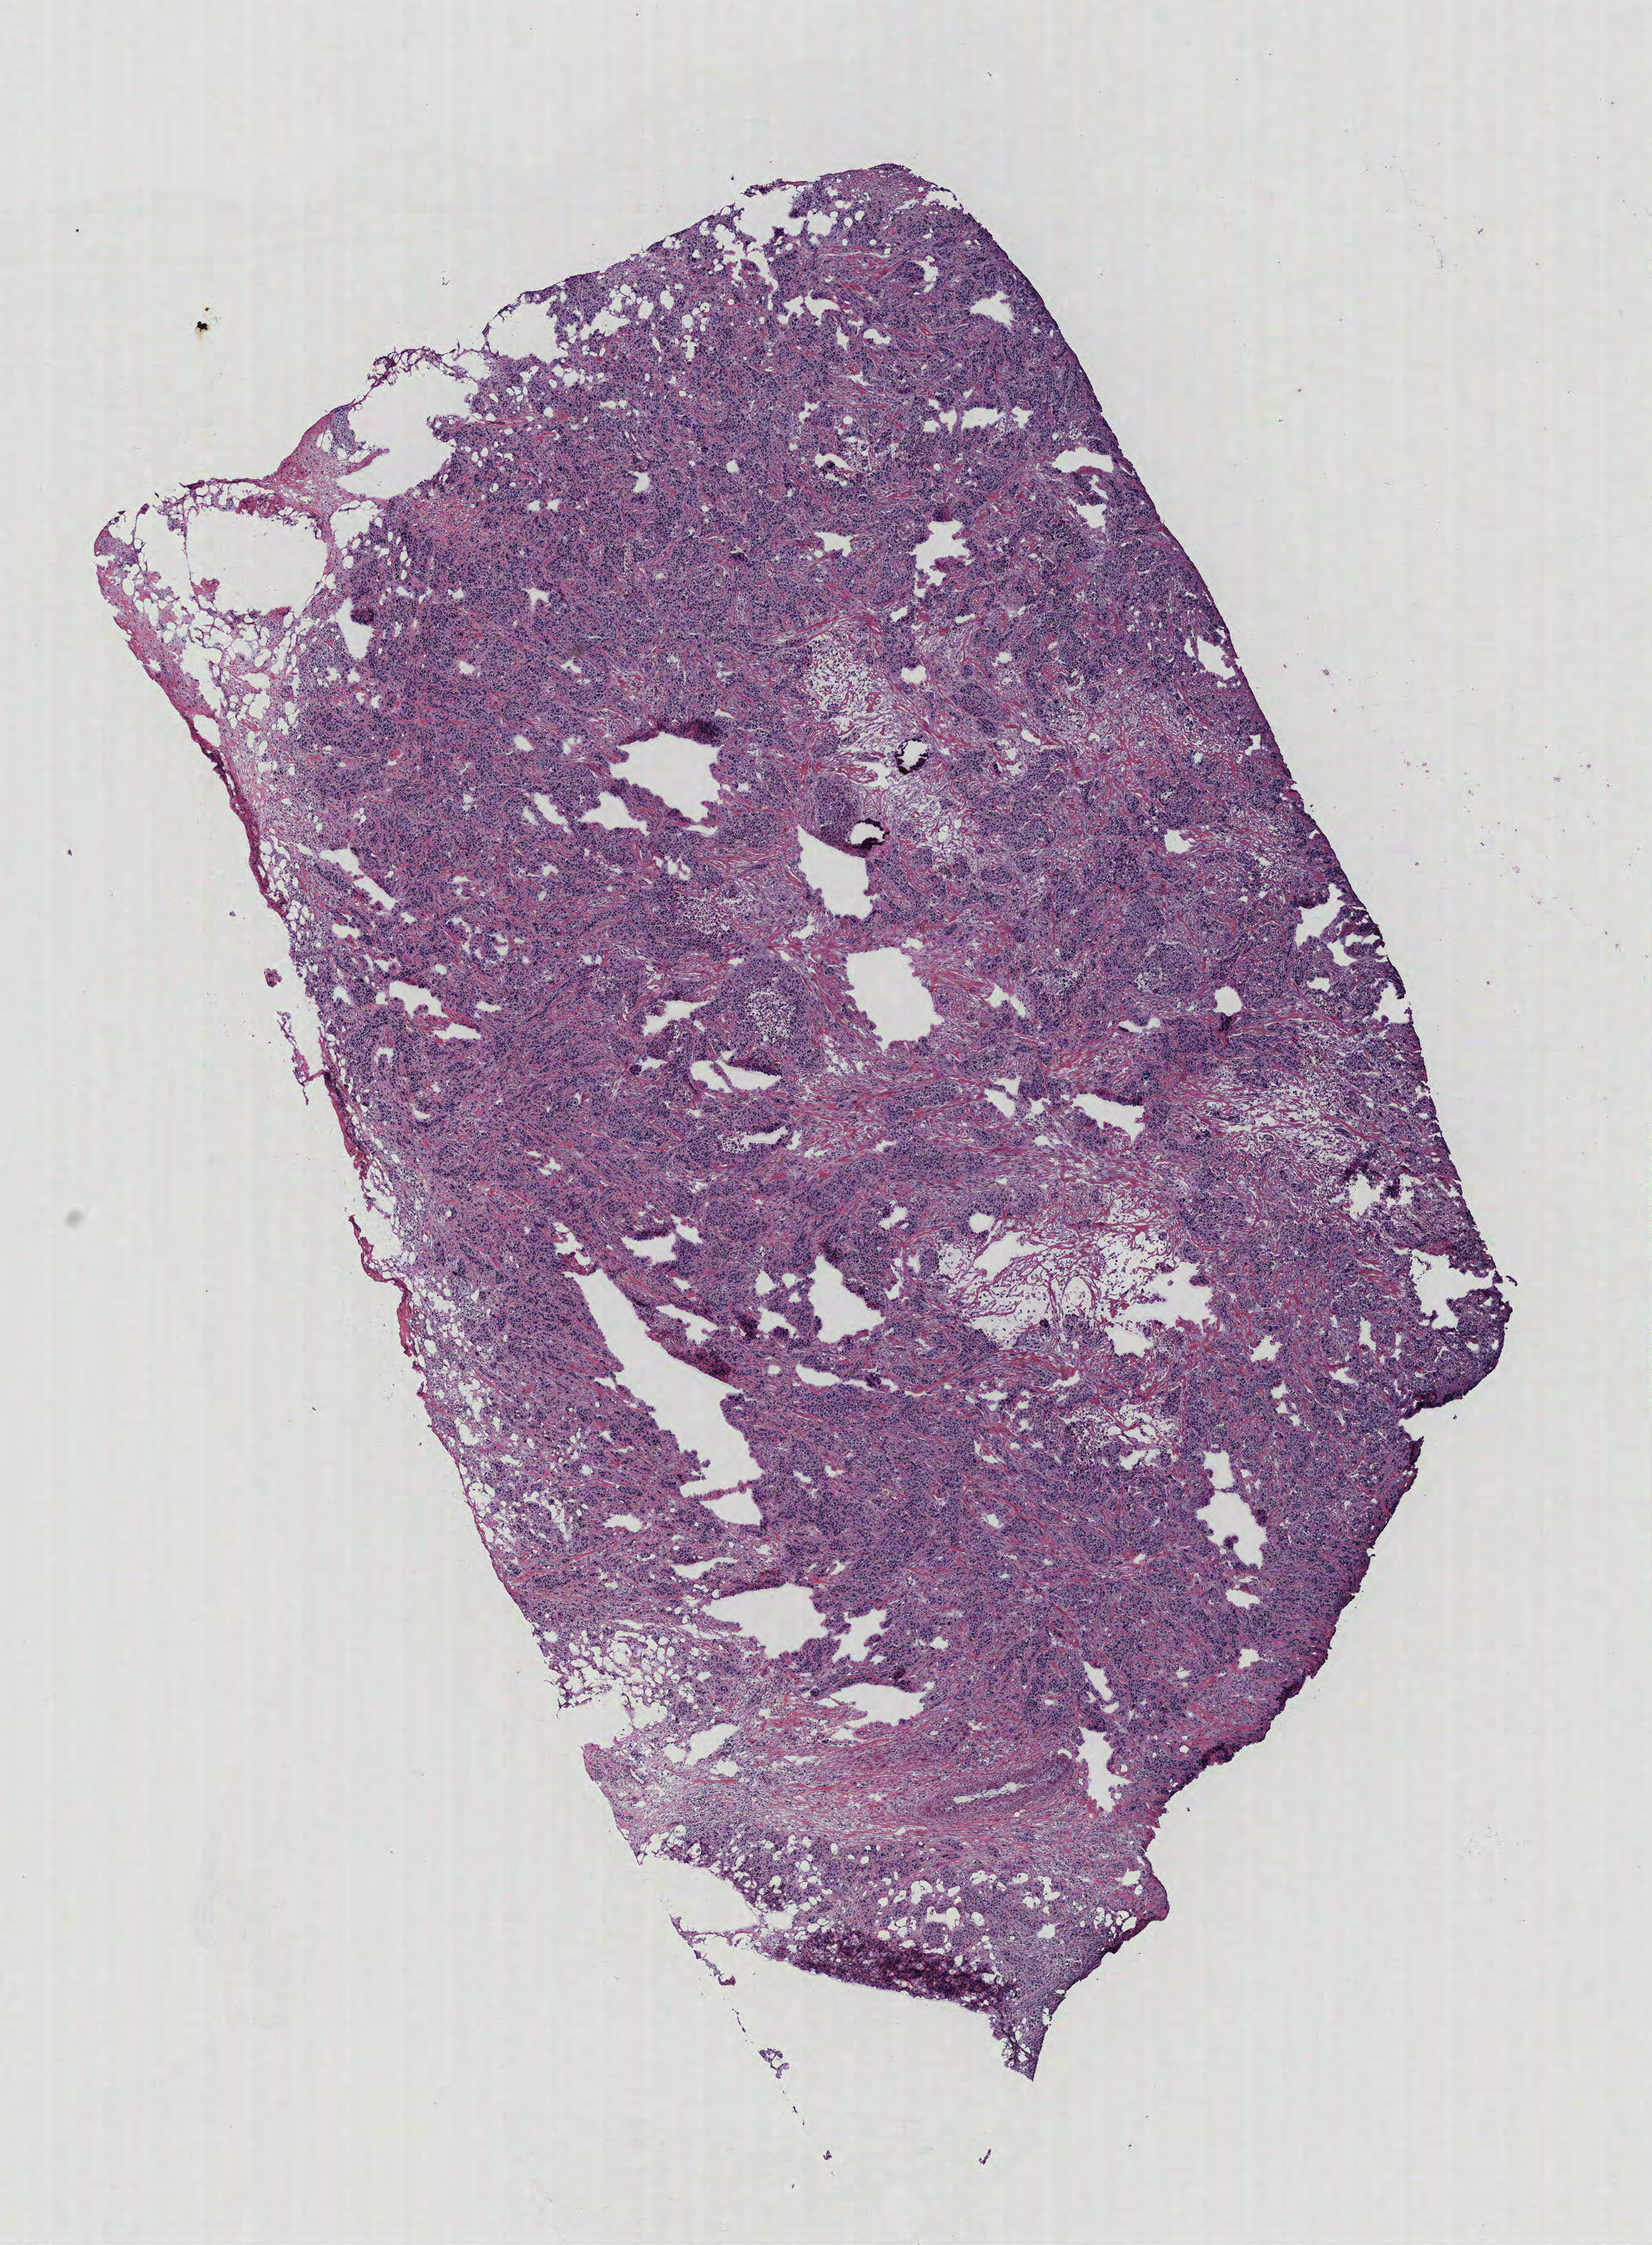
H&E-stained whole-slide image, a low-resolution overview of the entire scanned area, about 7.9 x 10.8 mm (from a 40x scan). Tumour tissue sample, breast. 47-year-old female patient.
Histologic diagnosis: Infiltrating duct carcinoma, NOS.